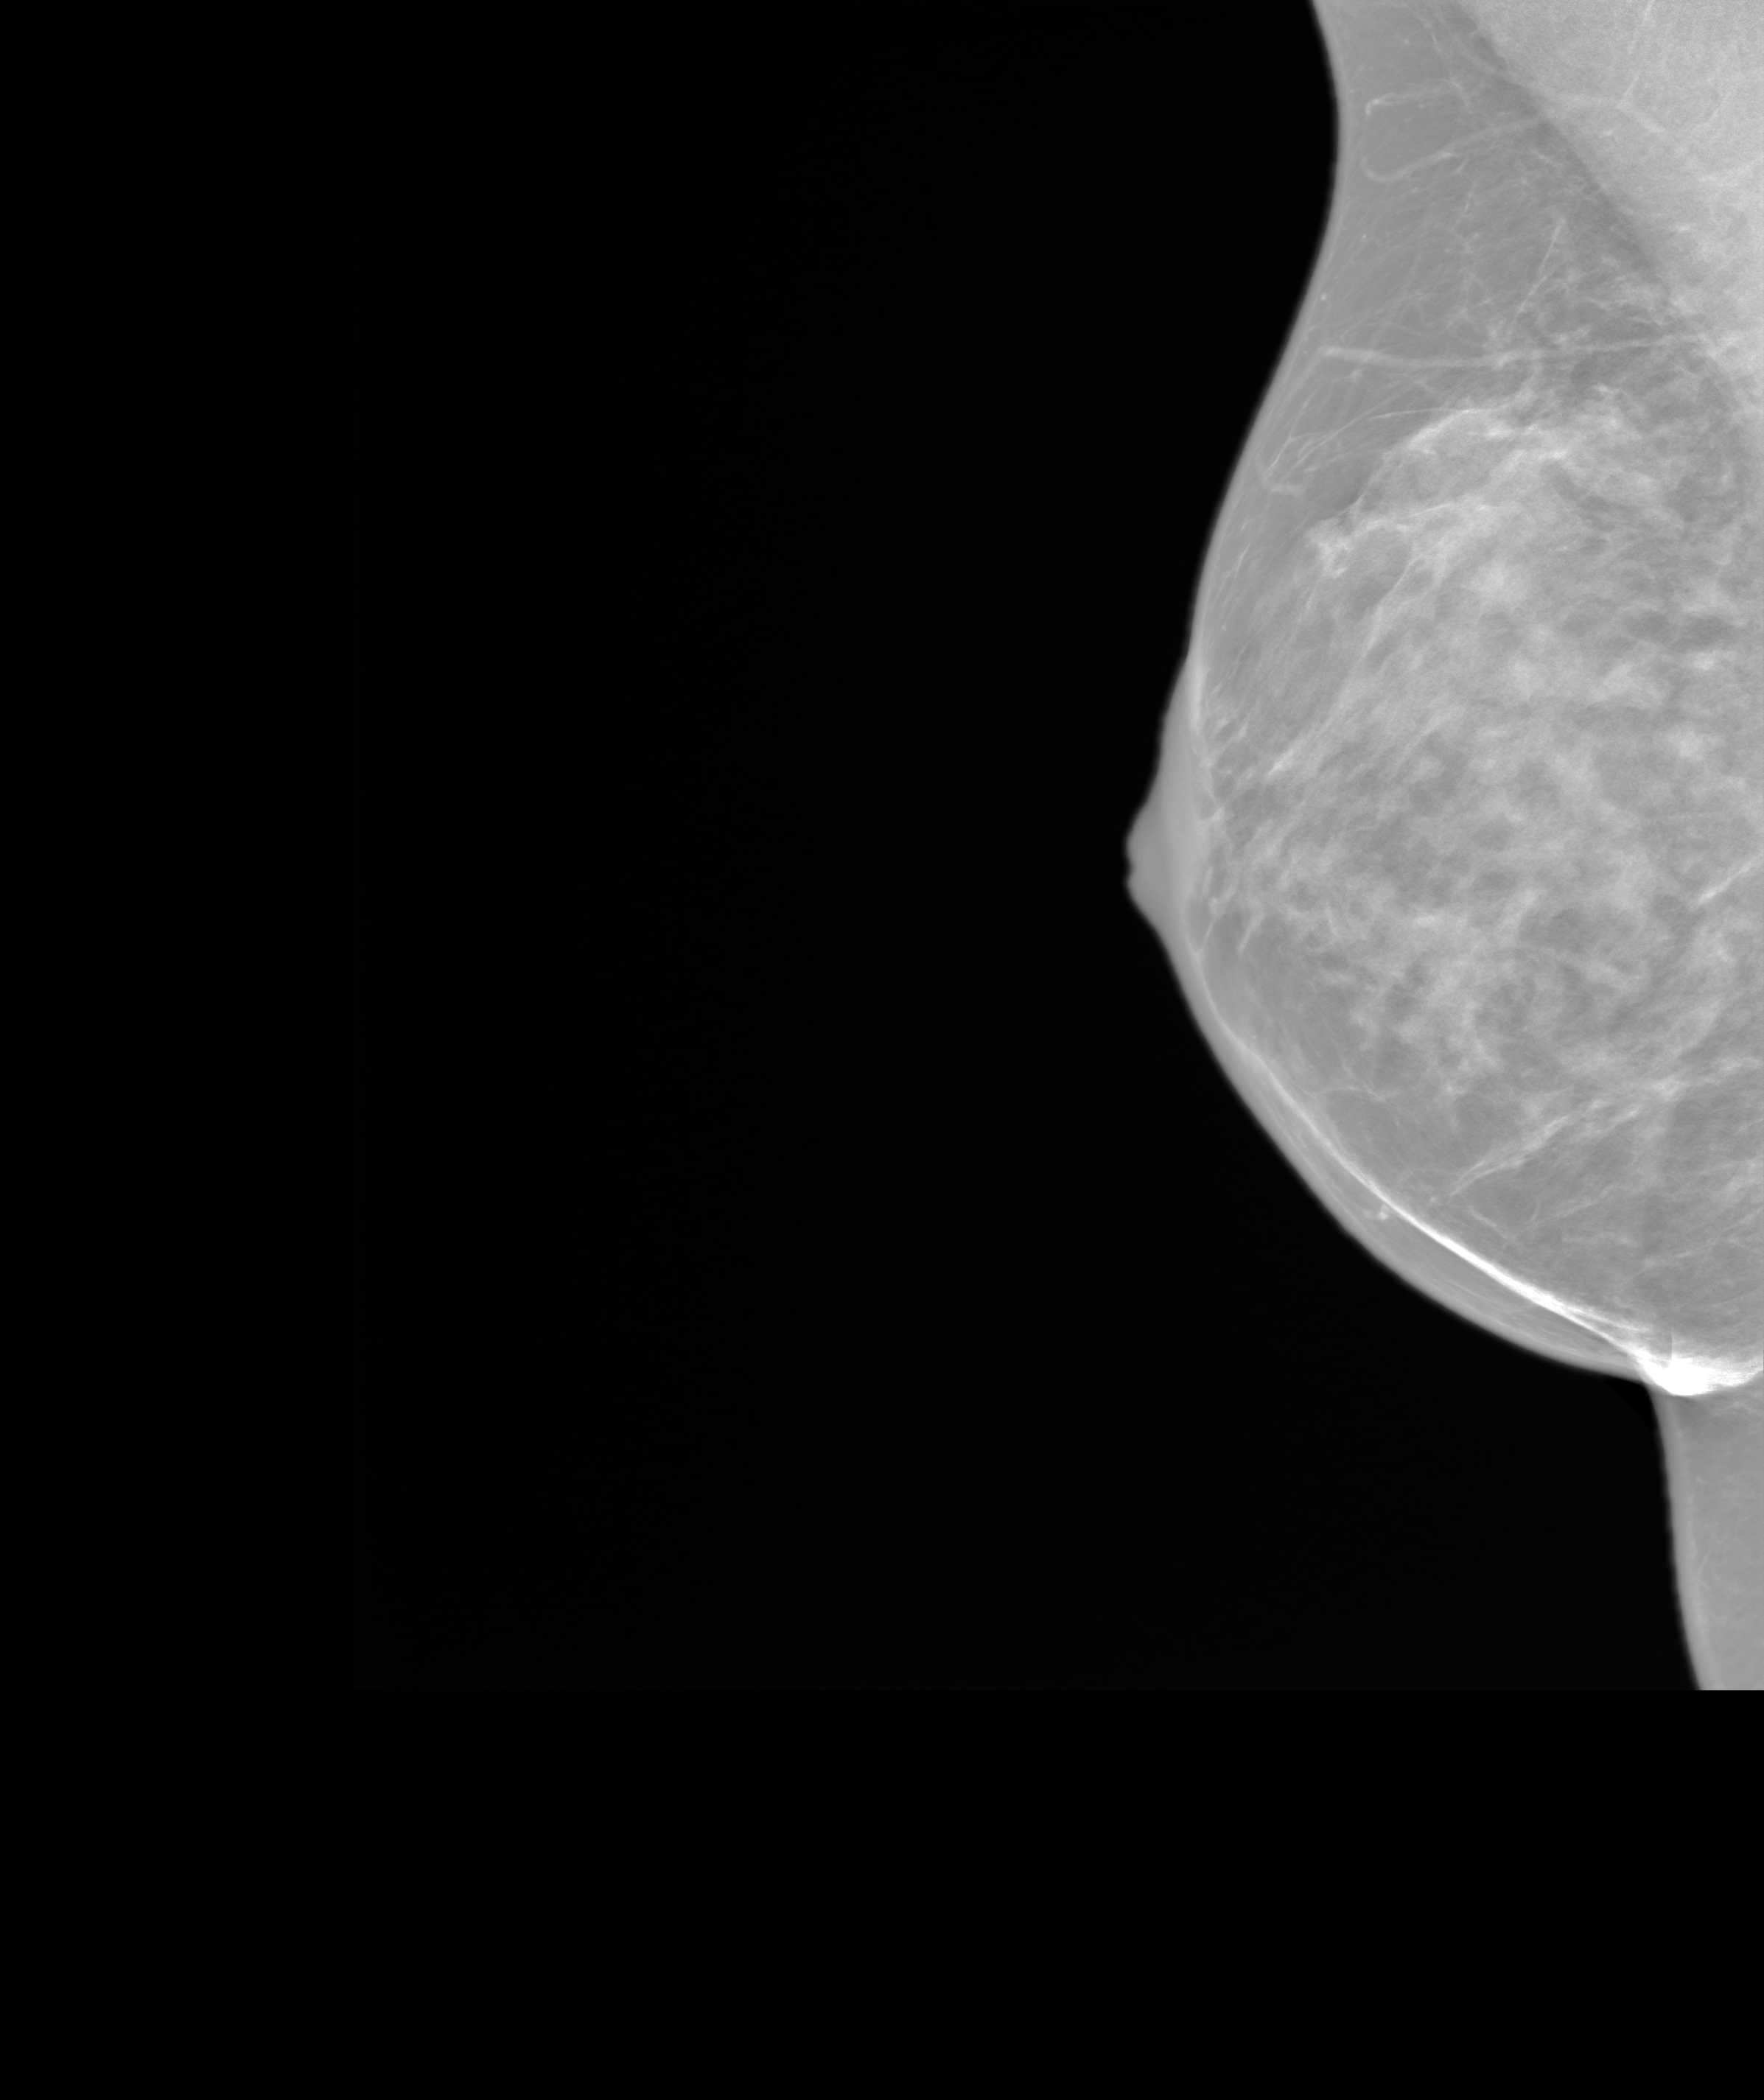
Screening examination. Patient: female, 43 years.
Image type: synthesized 2-D view from tomosynthesis. Breast: right. Projection: mediolateral oblique (MLO) view.